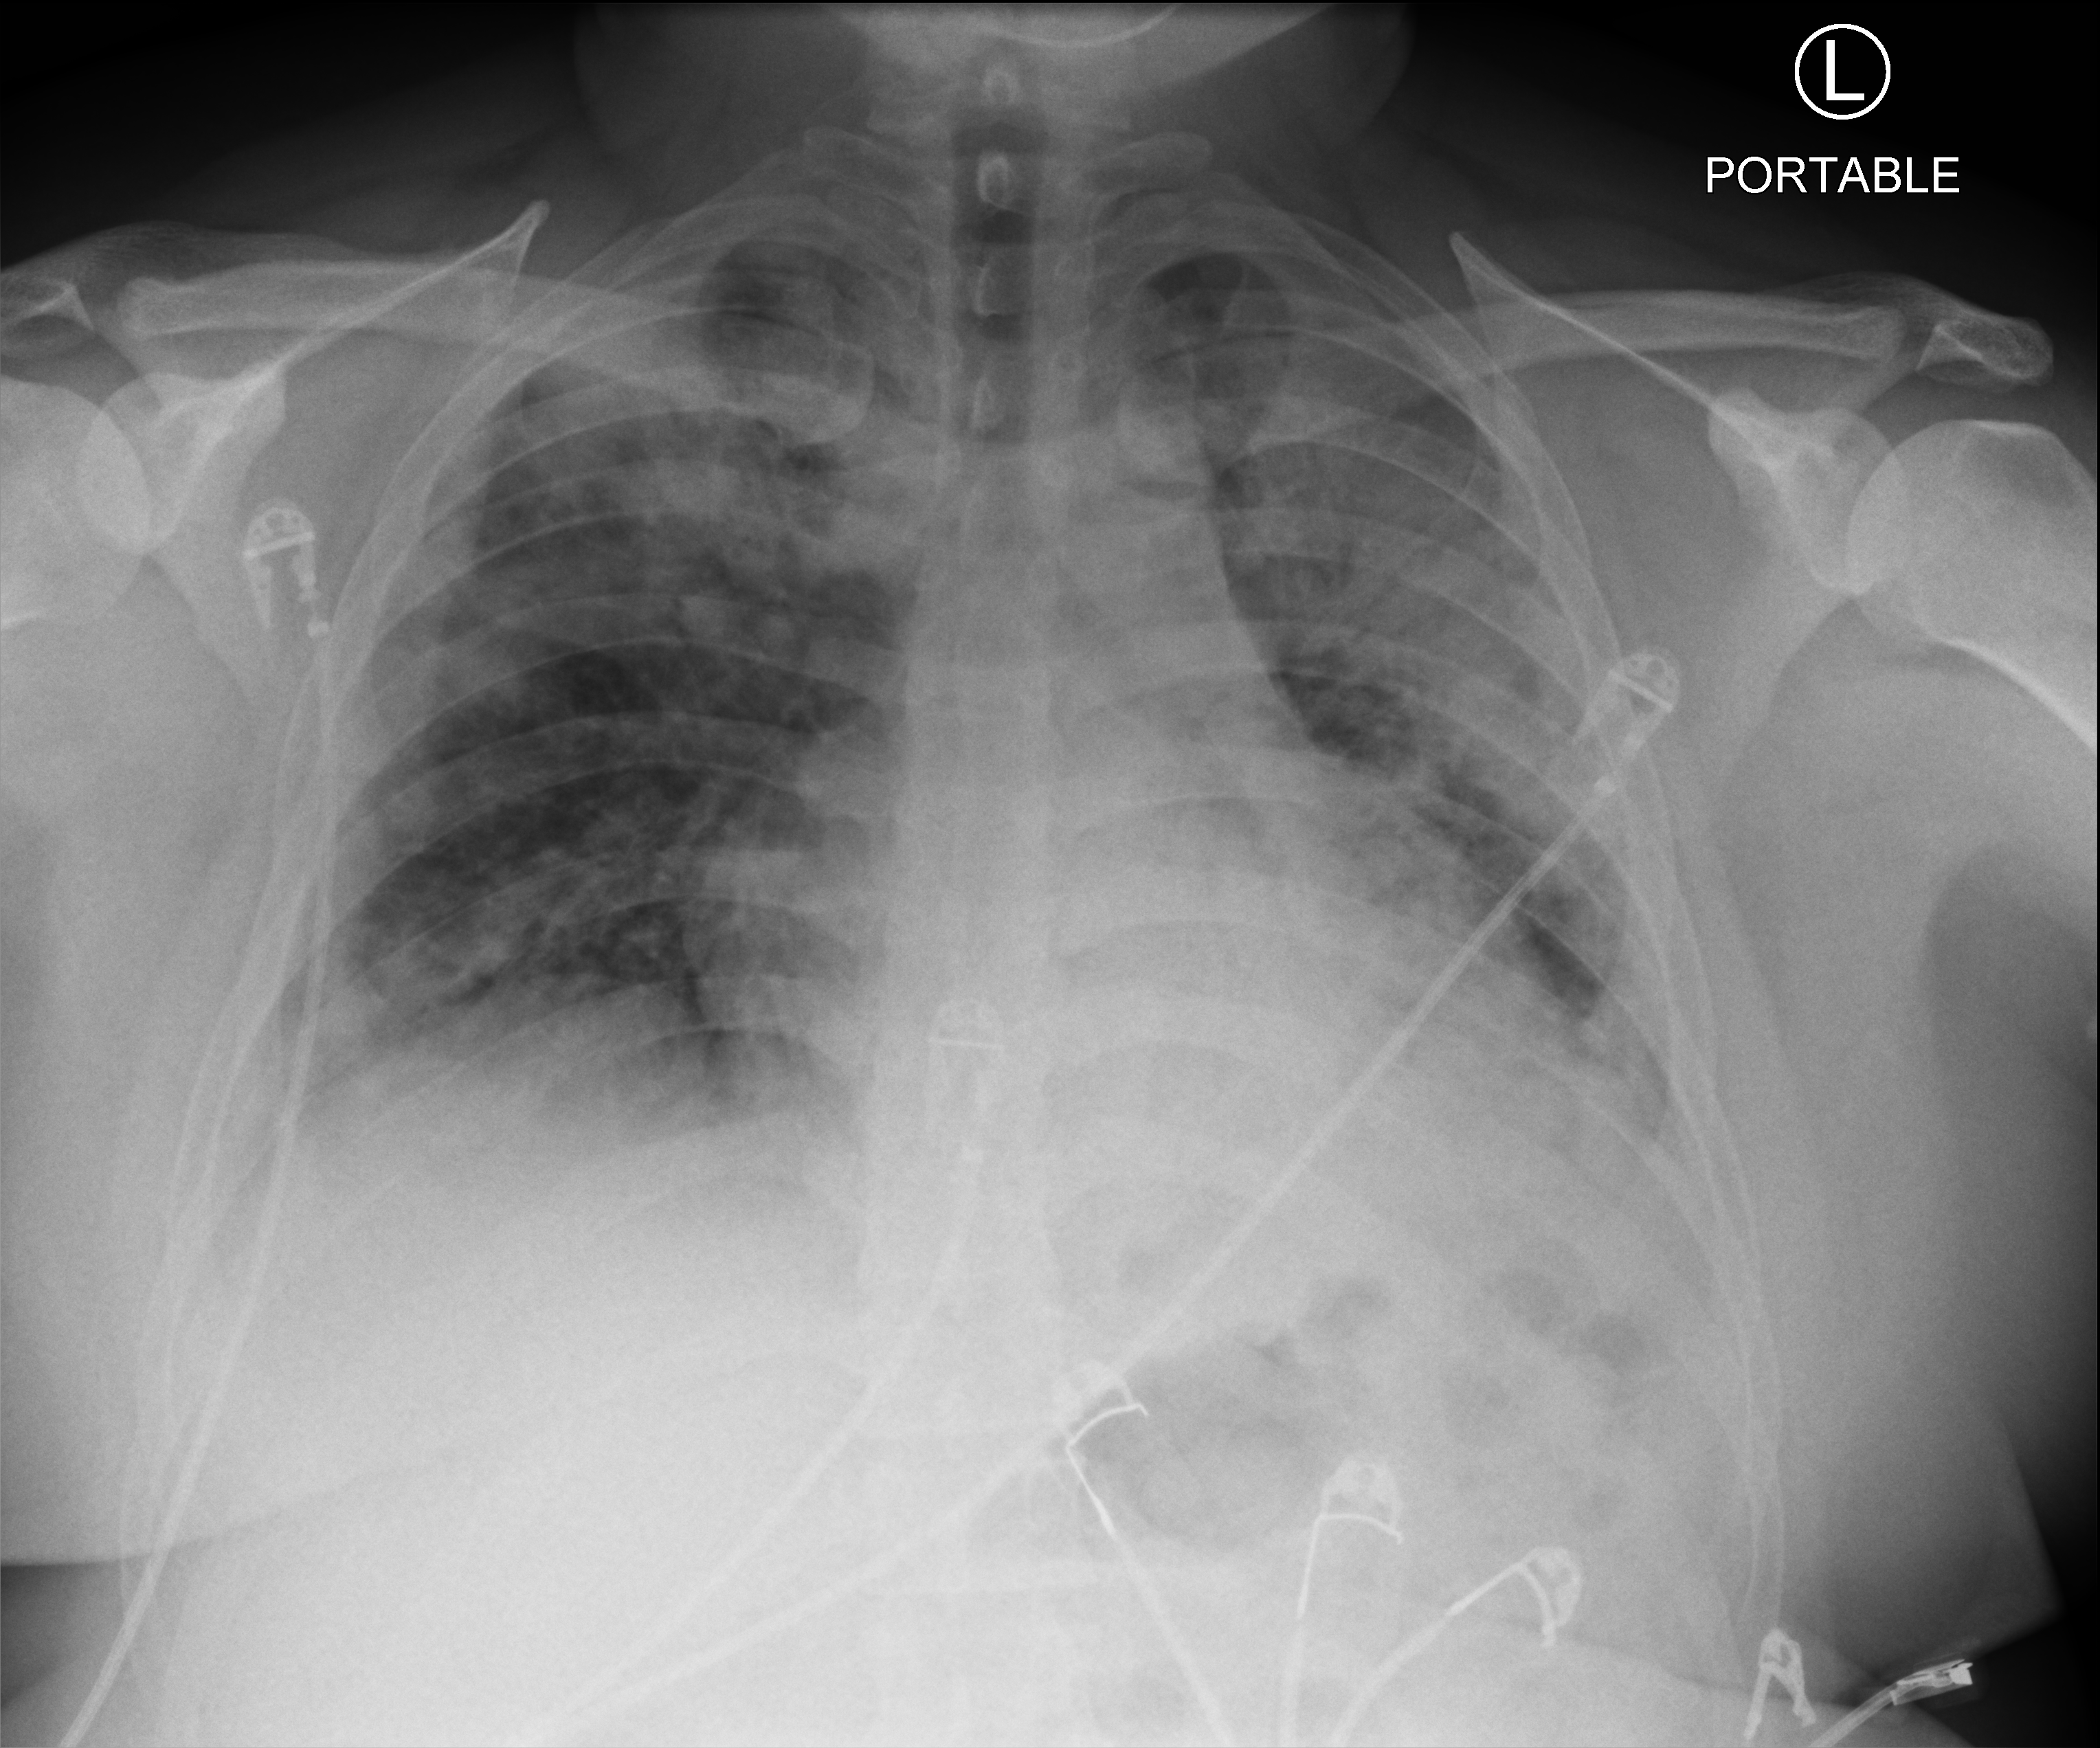
Chest X-ray (portable). Male patient hospitalised with COVID-19, age 18–59 years.
Hospital-stay facts (about this admission, not read from this image; timing relative to this image not recorded): mechanically ventilated during this hospital stay: no; admitted to intensive care during this hospital stay: no.